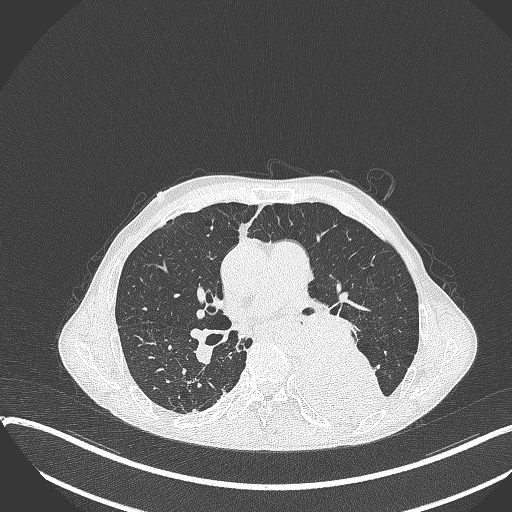
Chest CT, one axial slice; slice 205 of 401 in the series (ordered by position); reconstruction kernel B70f; lung window (W 1500 / L -600 HU); 1 mm slice thickness; 512 × 512 image matrix, field of view 400 × 400 mm. Male patient, age 57 years. Case-level facts recorded for this patient, not image findings: clinical TNM (as recorded): T4 N0 M0.
Annotated regions visible in this slice (bounding box drawn by a radiologist):
- lung tumour (recorded histology: squamous cell carcinoma): bounding box <296,343,391,434> (left, top, right, bottom; pixels)